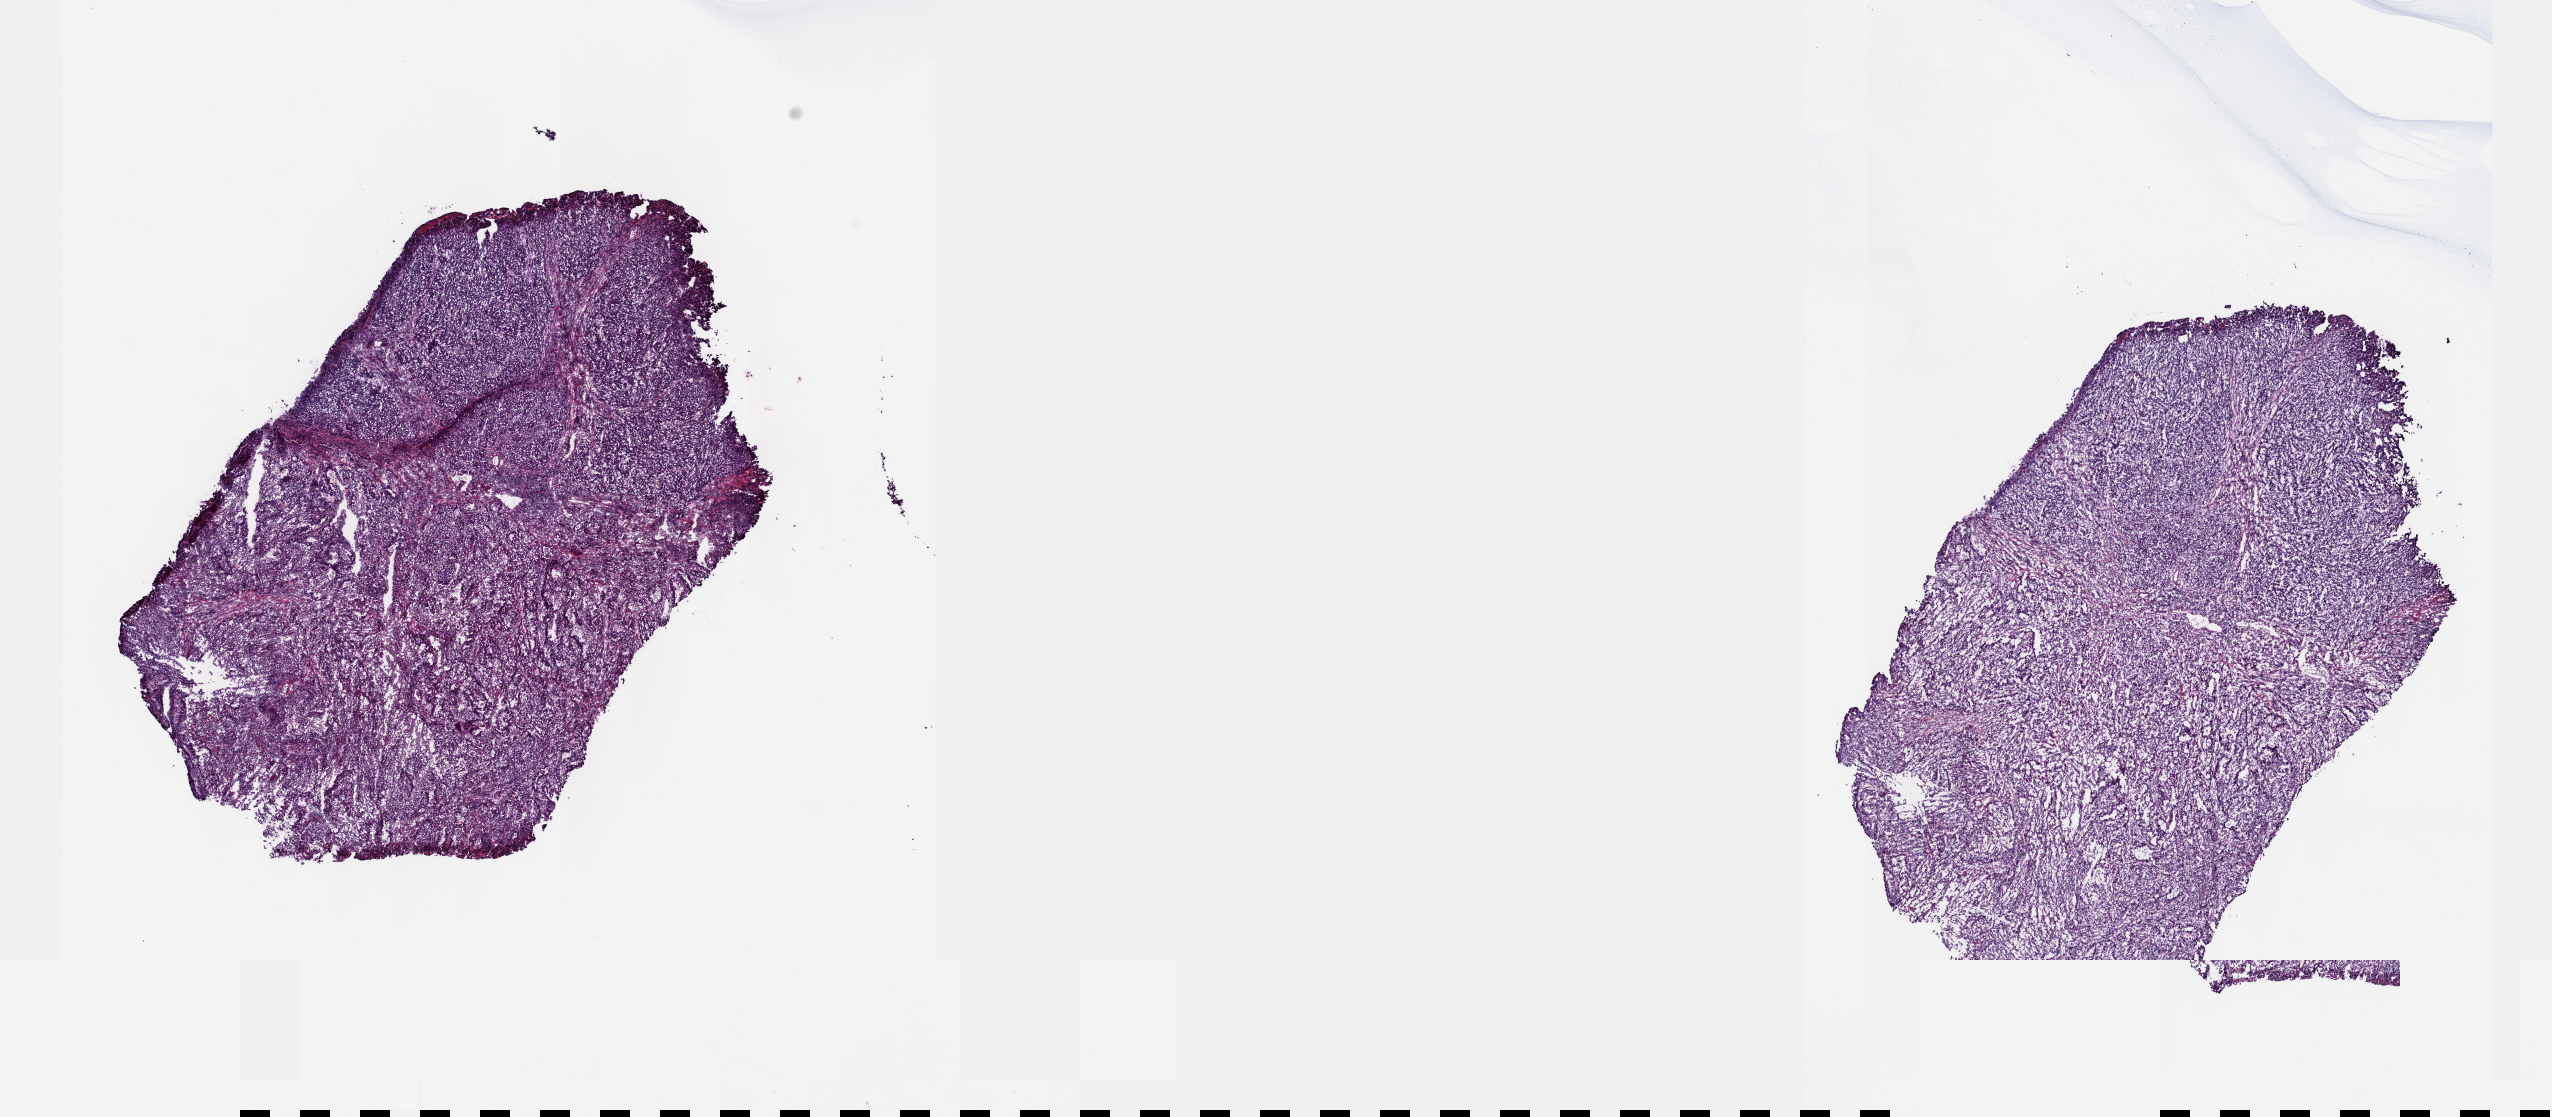
Whole-slide histology image, H&E, shown as a low-resolution overview of the whole scanned area (about 20.6 x 9.0 mm, acquisition: 40x scan), frozen section from the top of the tissue portion, primary tumour sample from the stomach. Male, age 35 years at initial diagnosis. Histologic grade: G2 (moderately differentiated). Composition of this section per pathologist review: tumour cells 70%, tumour nuclei 70%, normal cells 5%, stromal cells 25%, necrosis 0%. Inflammatory infiltration, as recorded: lymphocyte infiltration 40%, monocyte infiltration 20%, neutrophil infiltration 20%.
Lymph nodes positive (case pathology): 6 of 37 examined. AJCC pathologic stage: IIIA (7th edition). Histologic diagnosis: Adenocarcinoma, NOS (cardia, NOS).